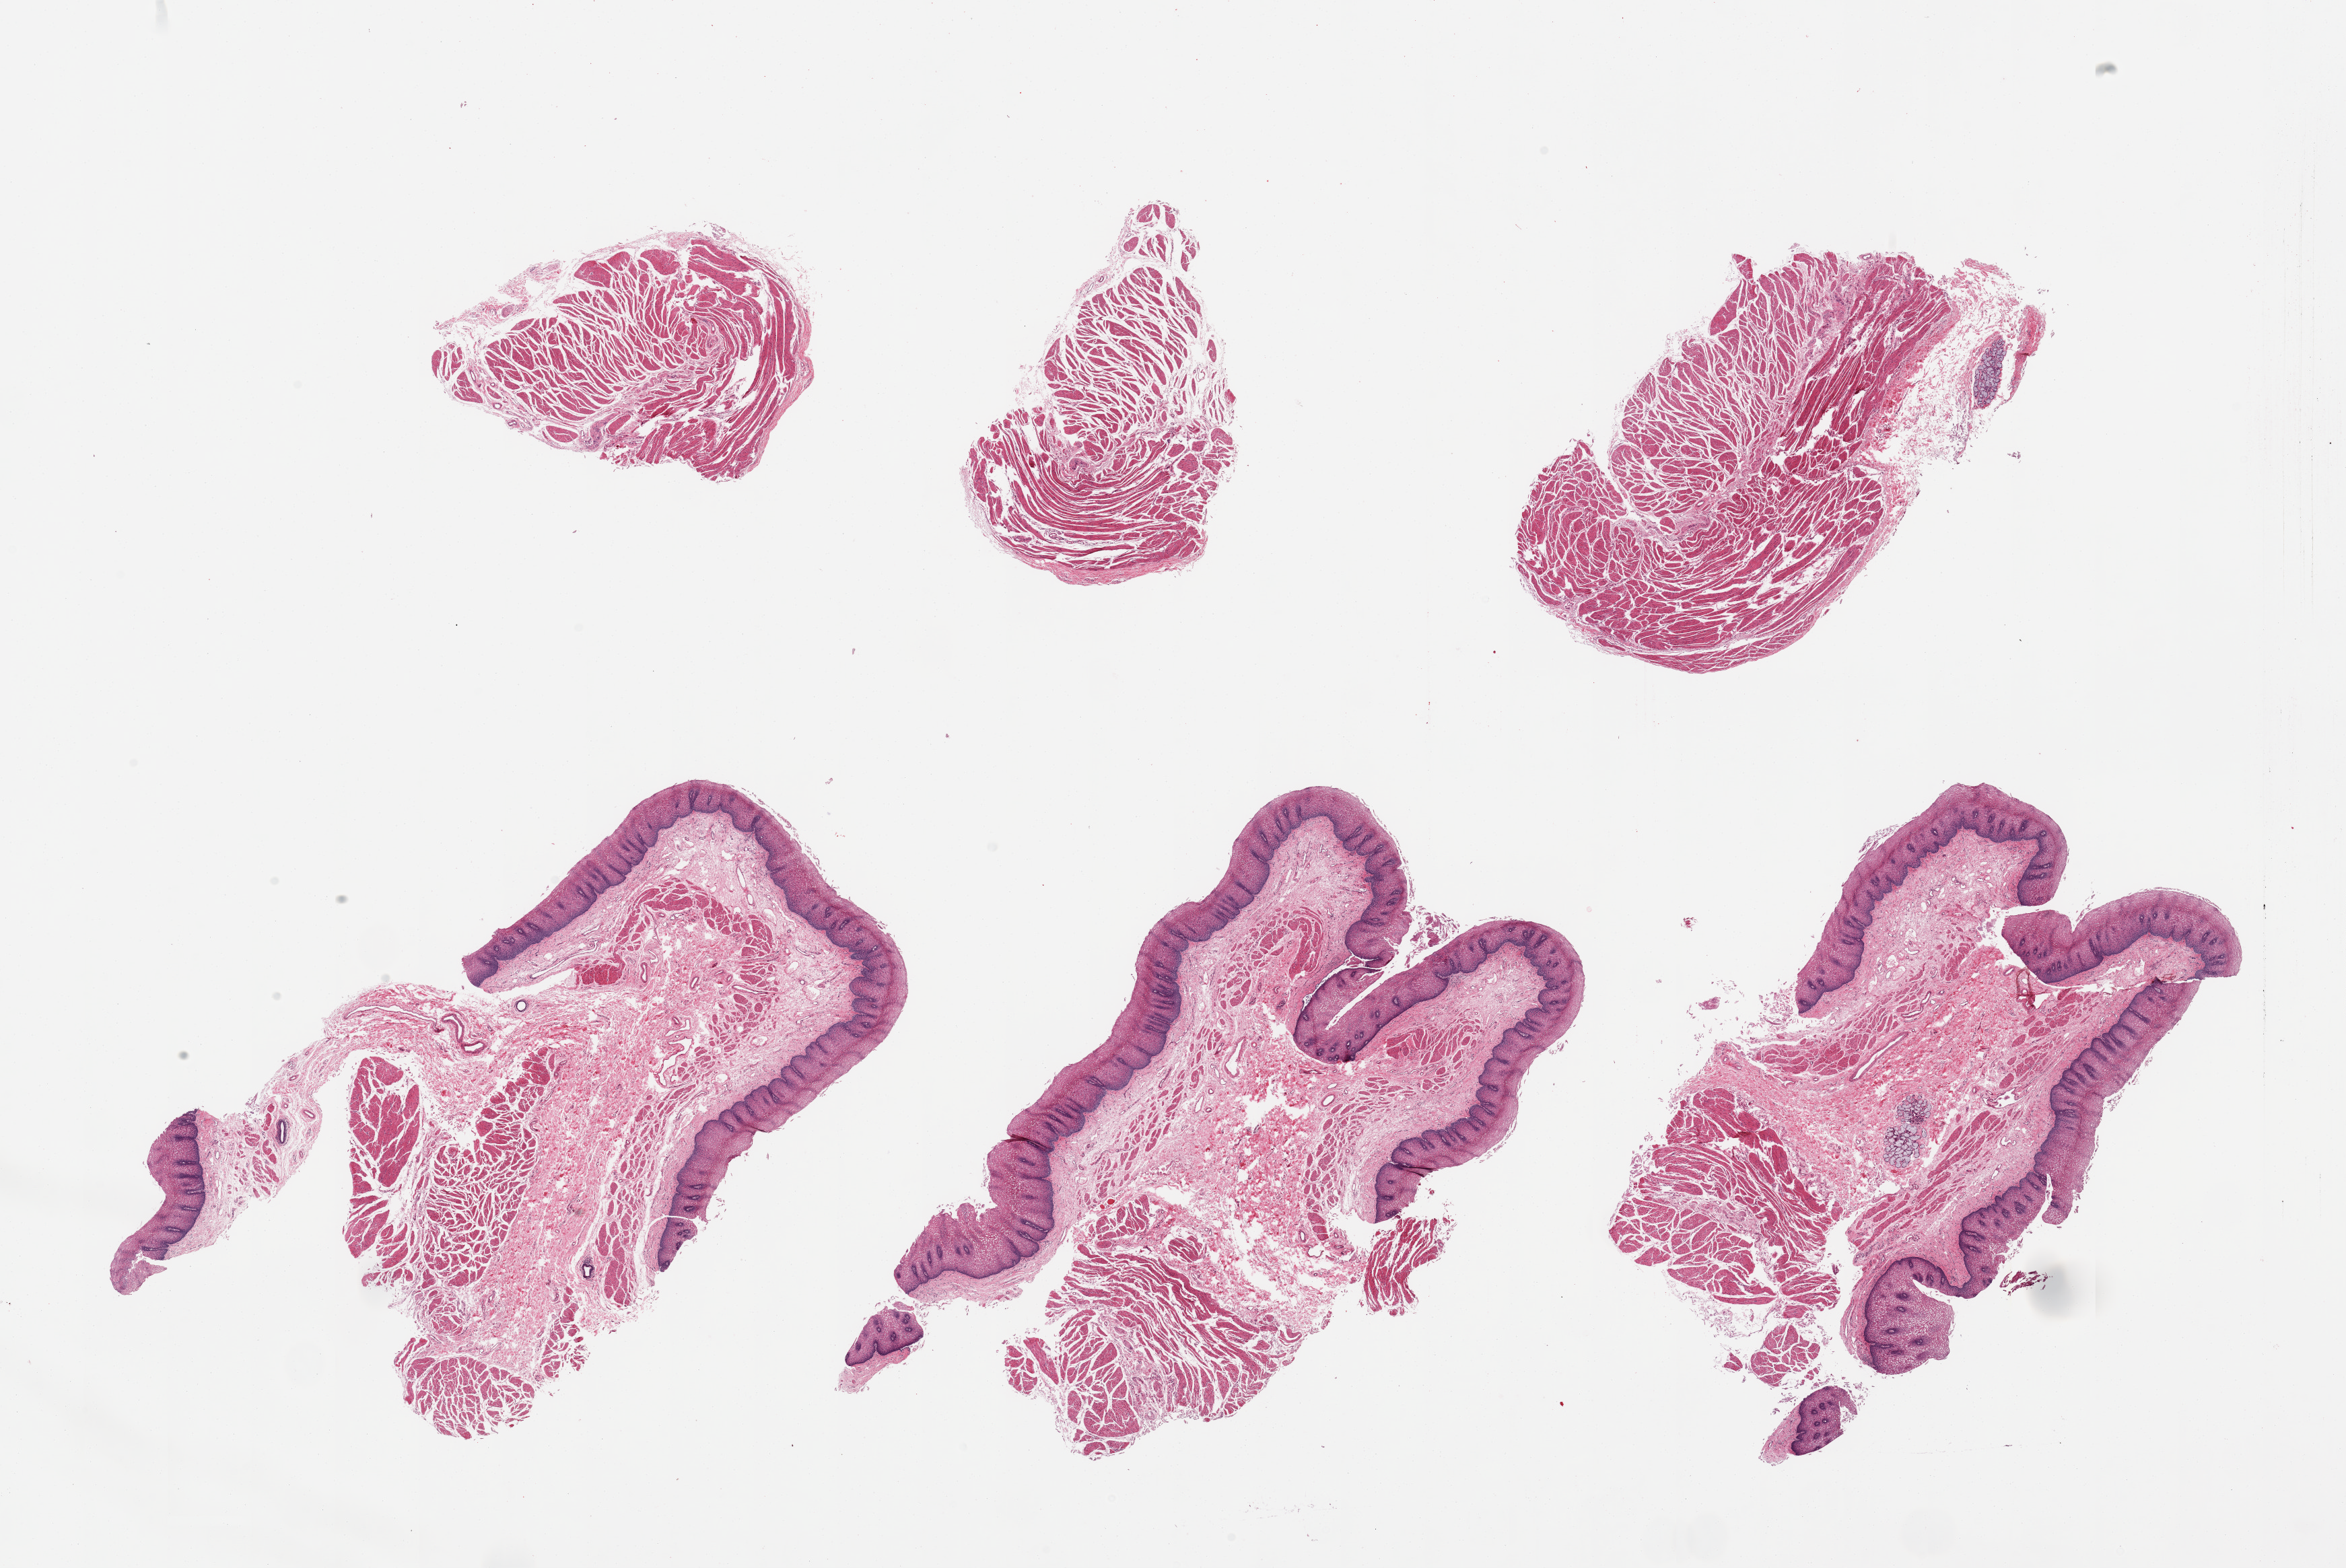
Digitized haematoxylin and eosin-stained section — a low-resolution overview of the entire scanned area, about 27.6 x 18.4 mm. PAXgene-fixed paraffin-embedded (PFPE) section. Sampled site (target tissue): esophageal mucous membrane. Donor tissue sample. Male donor.
Review note (as recorded): 6 pieces; 3 are muscularis, 3 are mucosa with portion of muscularis.